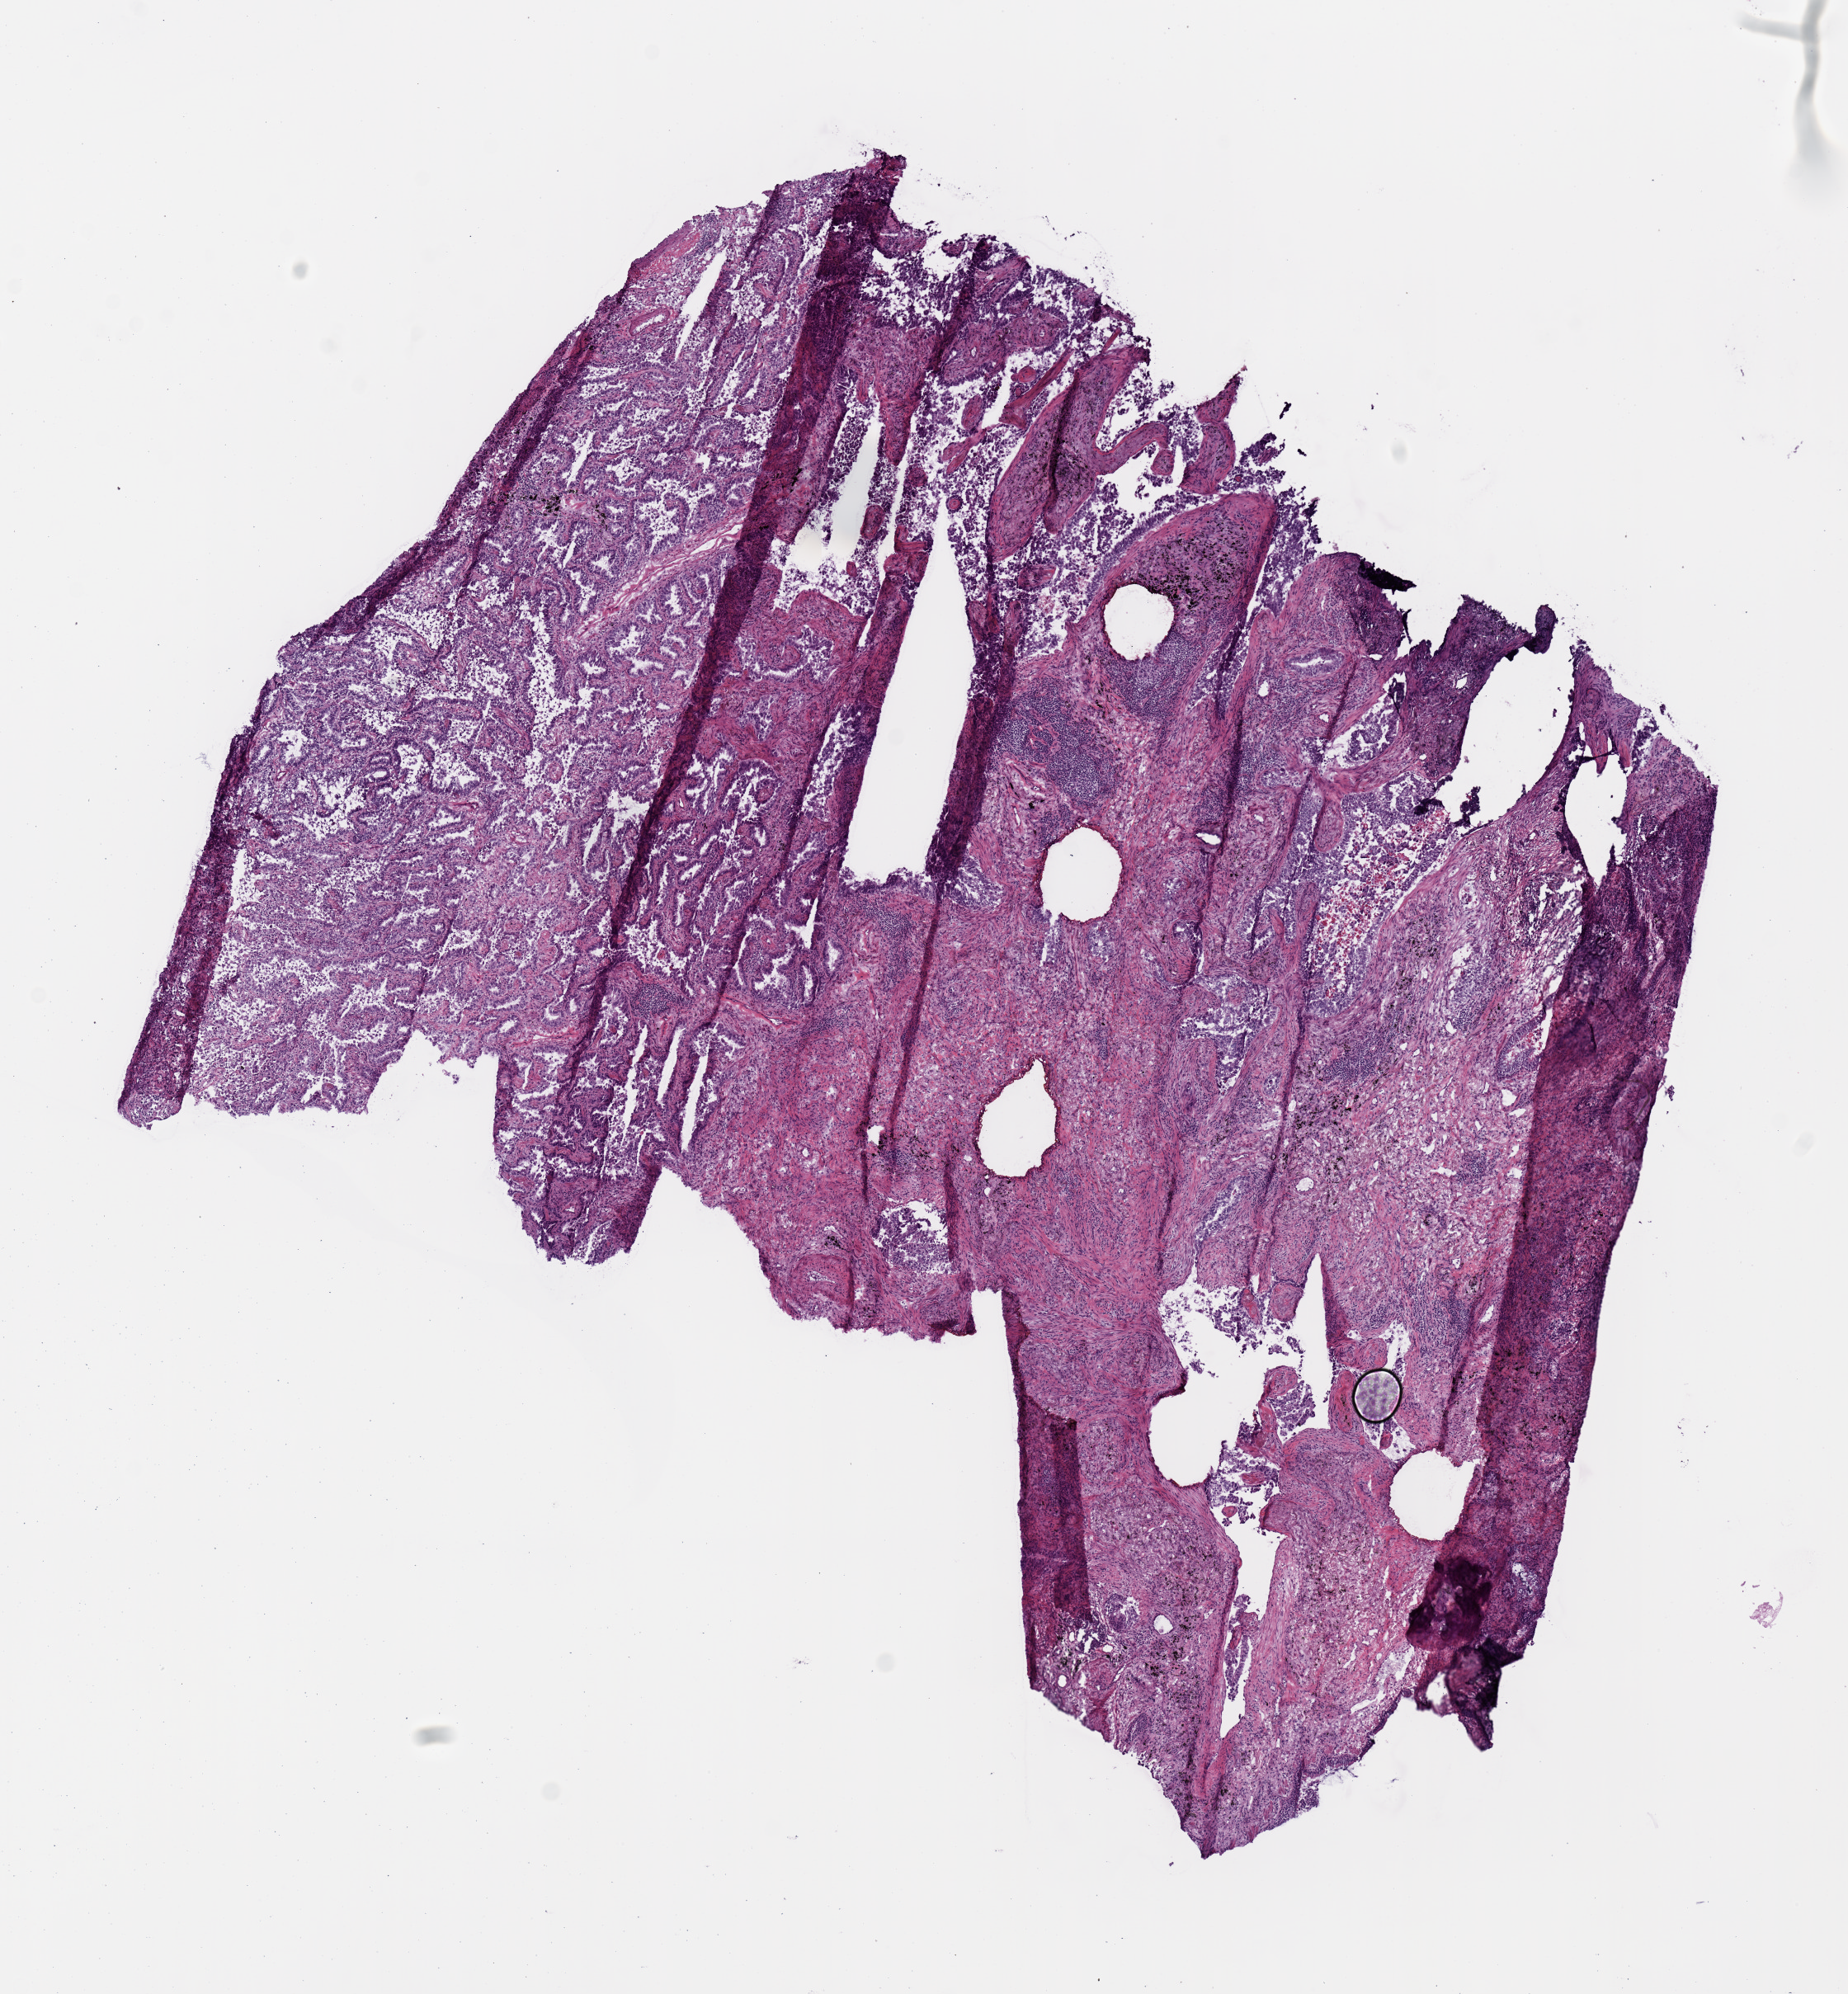
Digitized H&E-stained tissue section (whole slide), a low-resolution overview of the entire scanned area, about 8.9 x 9.6 mm (slide scanned at 20x), frozen section from the top of the tissue portion, primary tumour sample from the lung. Female, age 70 years at initial diagnosis. Composition of this section per pathologist review: tumour cells 100%, tumour nuclei 80%, normal cells 0%, stromal cells 0%, necrosis 0%. Inflammatory infiltration, as recorded: lymphocyte infiltration 7%, monocyte infiltration 4%, neutrophil infiltration 0%.
- laterality: right
- AJCC pathologic stage: I (7th edition)
- TNM: T1b N0 M0
- pathologic diagnosis: Acinar cell carcinoma (upper lobe, lung)